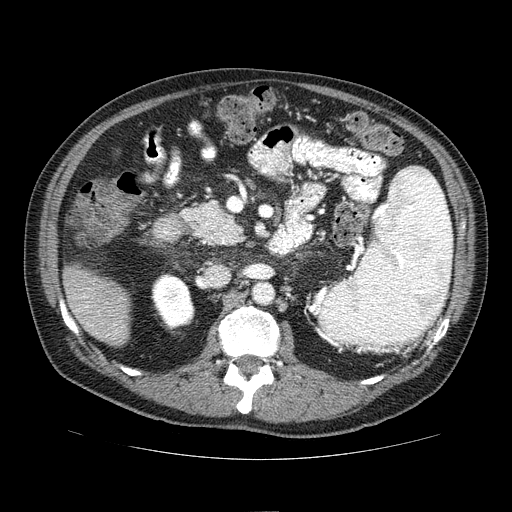
Contrast-enhanced abdominal CT (liver protocol), one axial slice; slice 23 of 81 in the series (ordered by position); reconstruction kernel STANDARD; 100 kVp; one of 2 acquisitions stored at this slice position; soft-tissue window (W 400 / L 40 HU); 2.5 mm slice thickness; 512 × 512 image matrix. Case-level facts recorded for this patient, not image findings: diagnosis: hepatocellular carcinoma (patient treated with transarterial chemoembolisation; whether this scan precedes or follows treatment is not stated here); TNM stage (as recorded): Stage-IIIA; Child-Pugh class: A; tumour differentiation: well differentiated; tumour nodularity: multinodular.
Outlined on this slice (semi-automatic segmentation, software-assisted and operator-edited):
- liver parenchyma outside the tumour (the mass and vessels are separate outlines, so this box may not span the whole liver): bounding box <62,264,130,346> (left, top, right, bottom; pixels)
- liver vessels: <74,296,116,336>